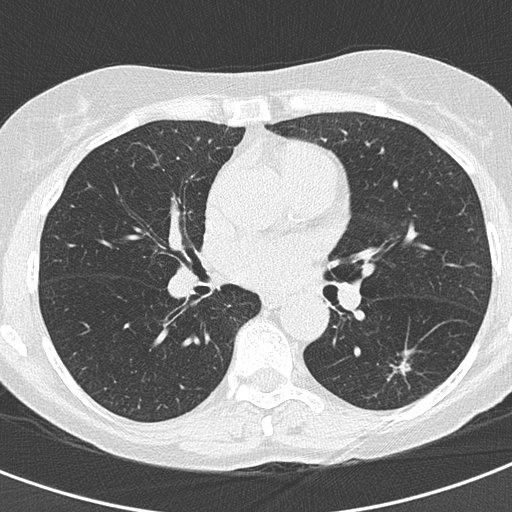
Chest CT (low-dose screening protocol), one axial image, second screening round (one year after baseline), lung window (W 1500 / L -600 HU), lung (sharp) reconstruction kernel (B50f). Female participant, aged 60 years at enrolment. Current smoker at enrolment.
Expert reader's lesion annotation, bounding box (x1, y1, x2, y2) in pixels: (378, 349, 415, 379). The exam's reader record, not a measurement of the box and not confirmed to be the same lesion: non-calcified nodule or mass ≥4 mm, left lower lobe, 10 × 9 mm, soft tissue attenuation. Official screen result: positive, other.